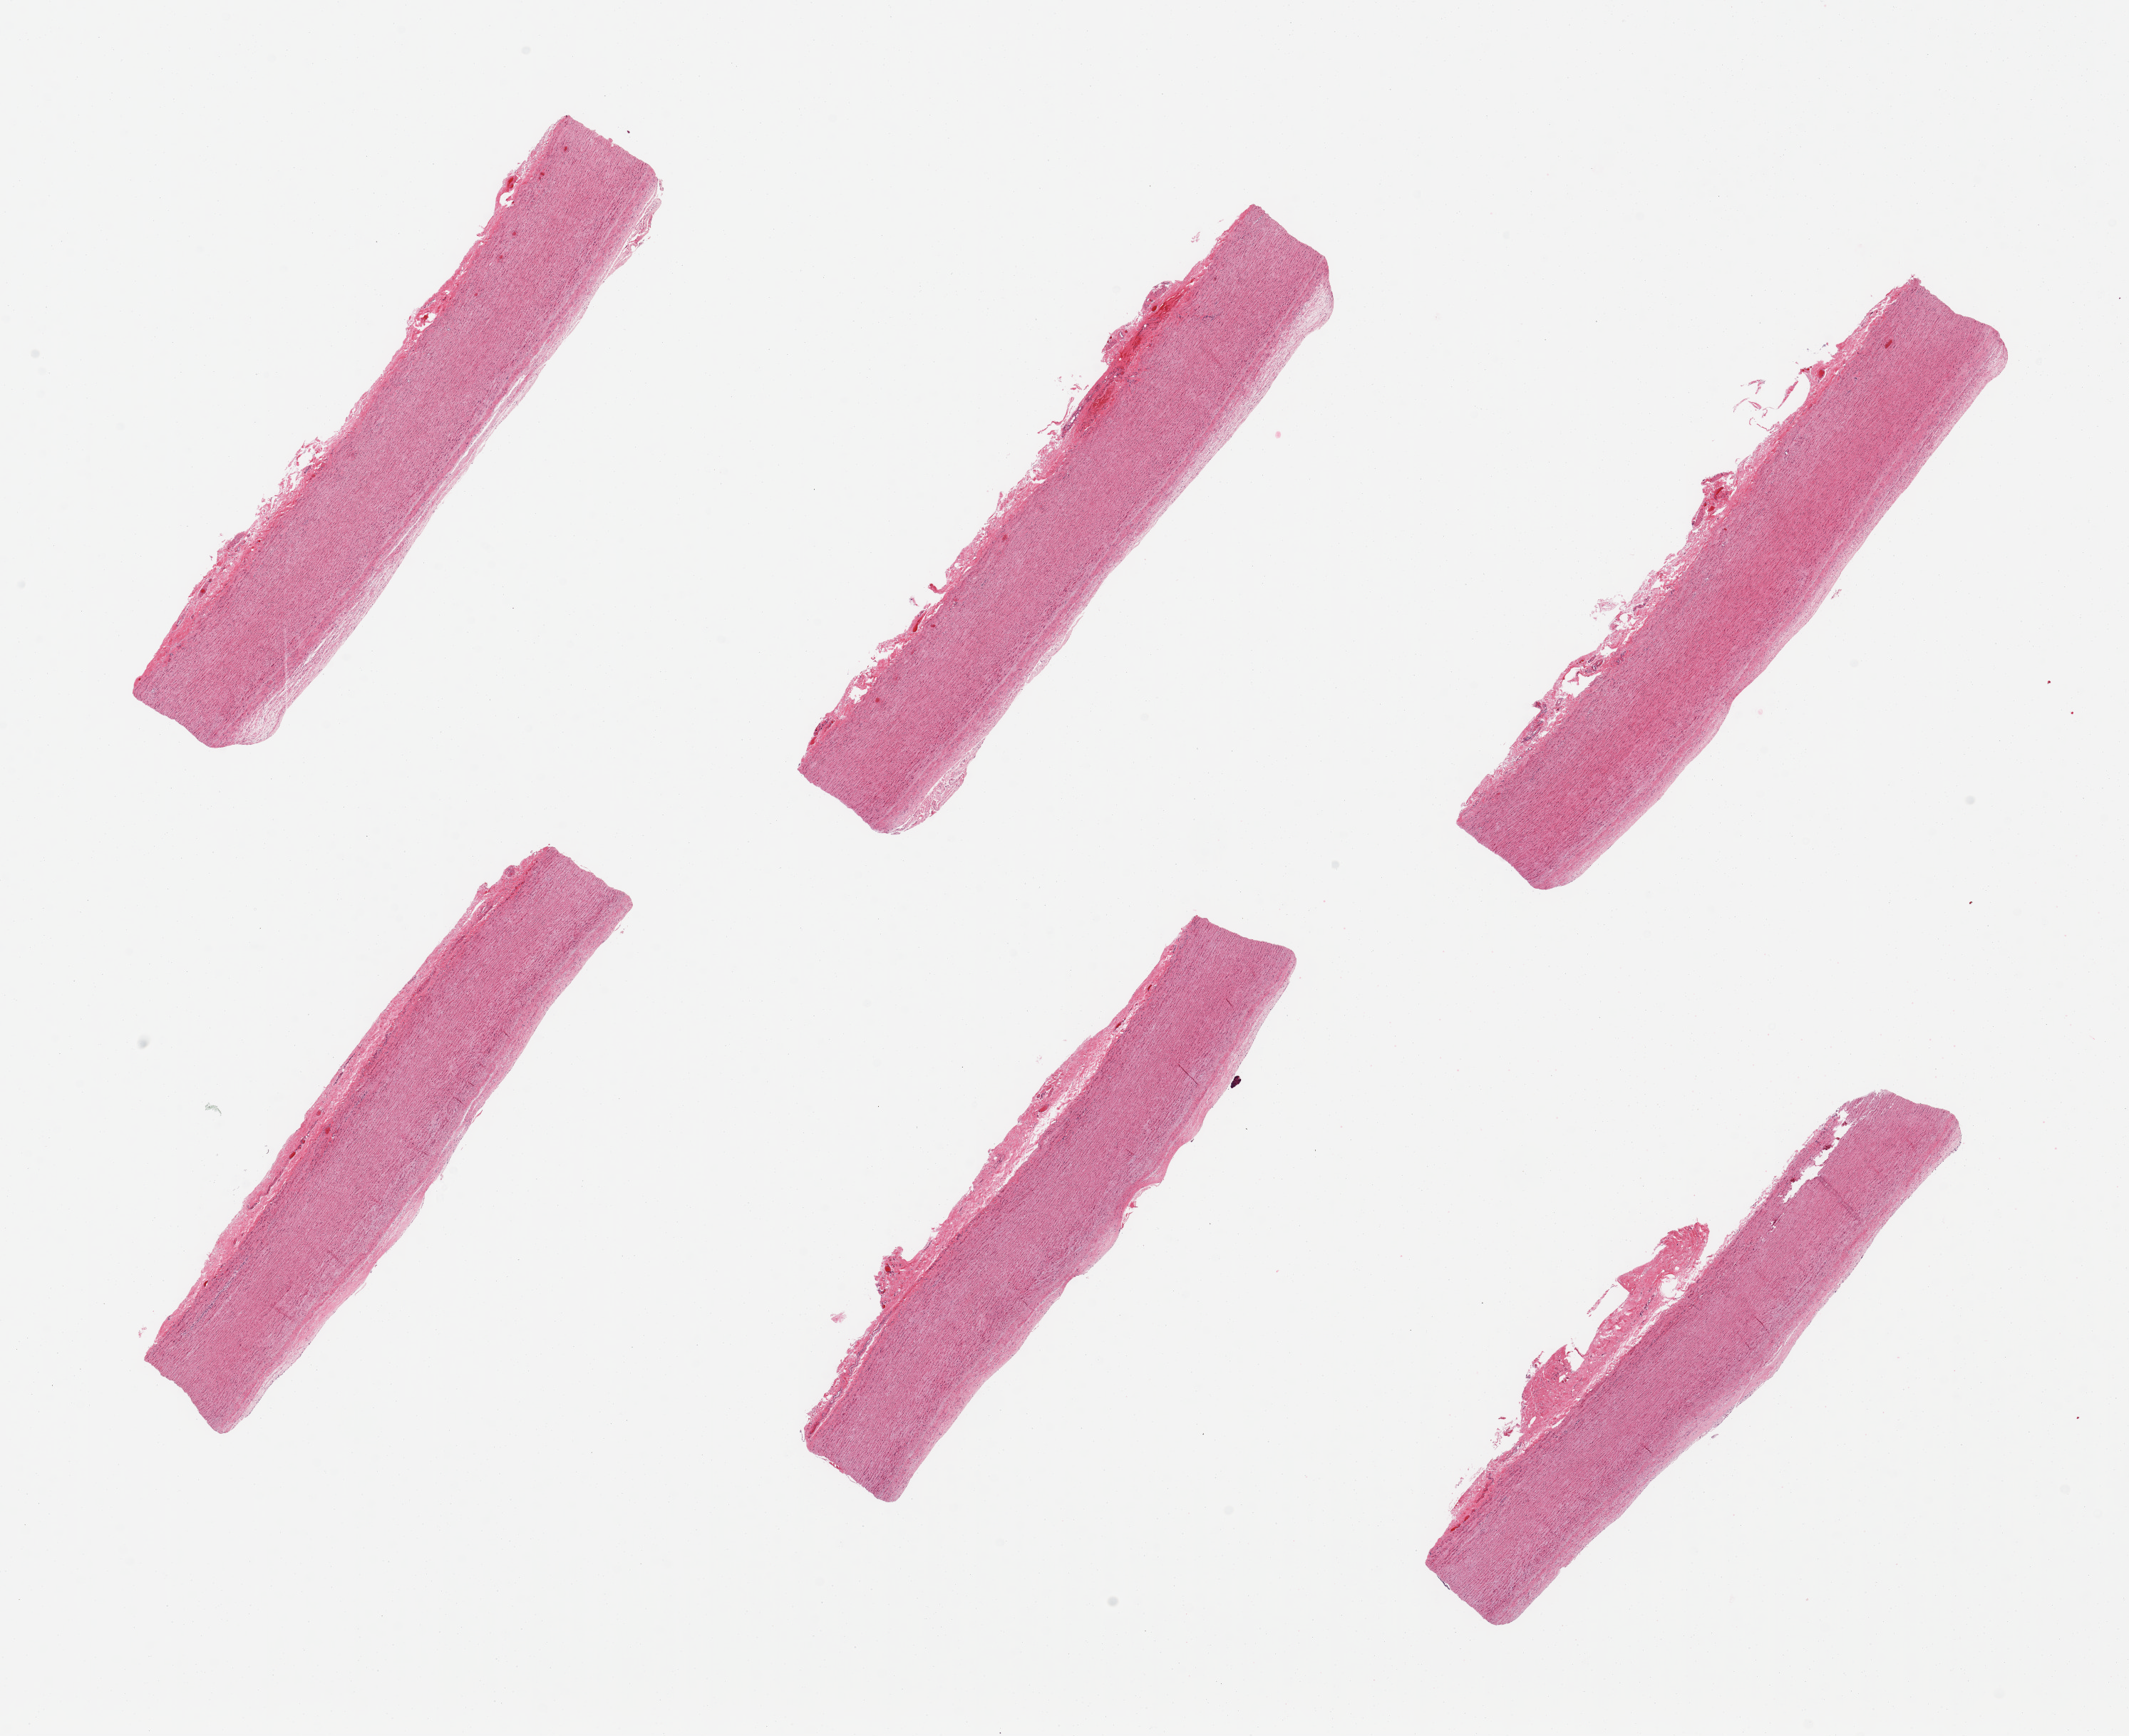
Whole-slide image, H&E stain — a low-resolution overview of the entire scanned area, about 23.6 x 19.3 mm; PAXgene-fixed, paraffin-embedded tissue; target tissue: aorta; tissue donor sample. Donor sex: female.
- reviewer comment on this tissue sample: 6 pieces; mild linear fibrous plaques; well trimmed